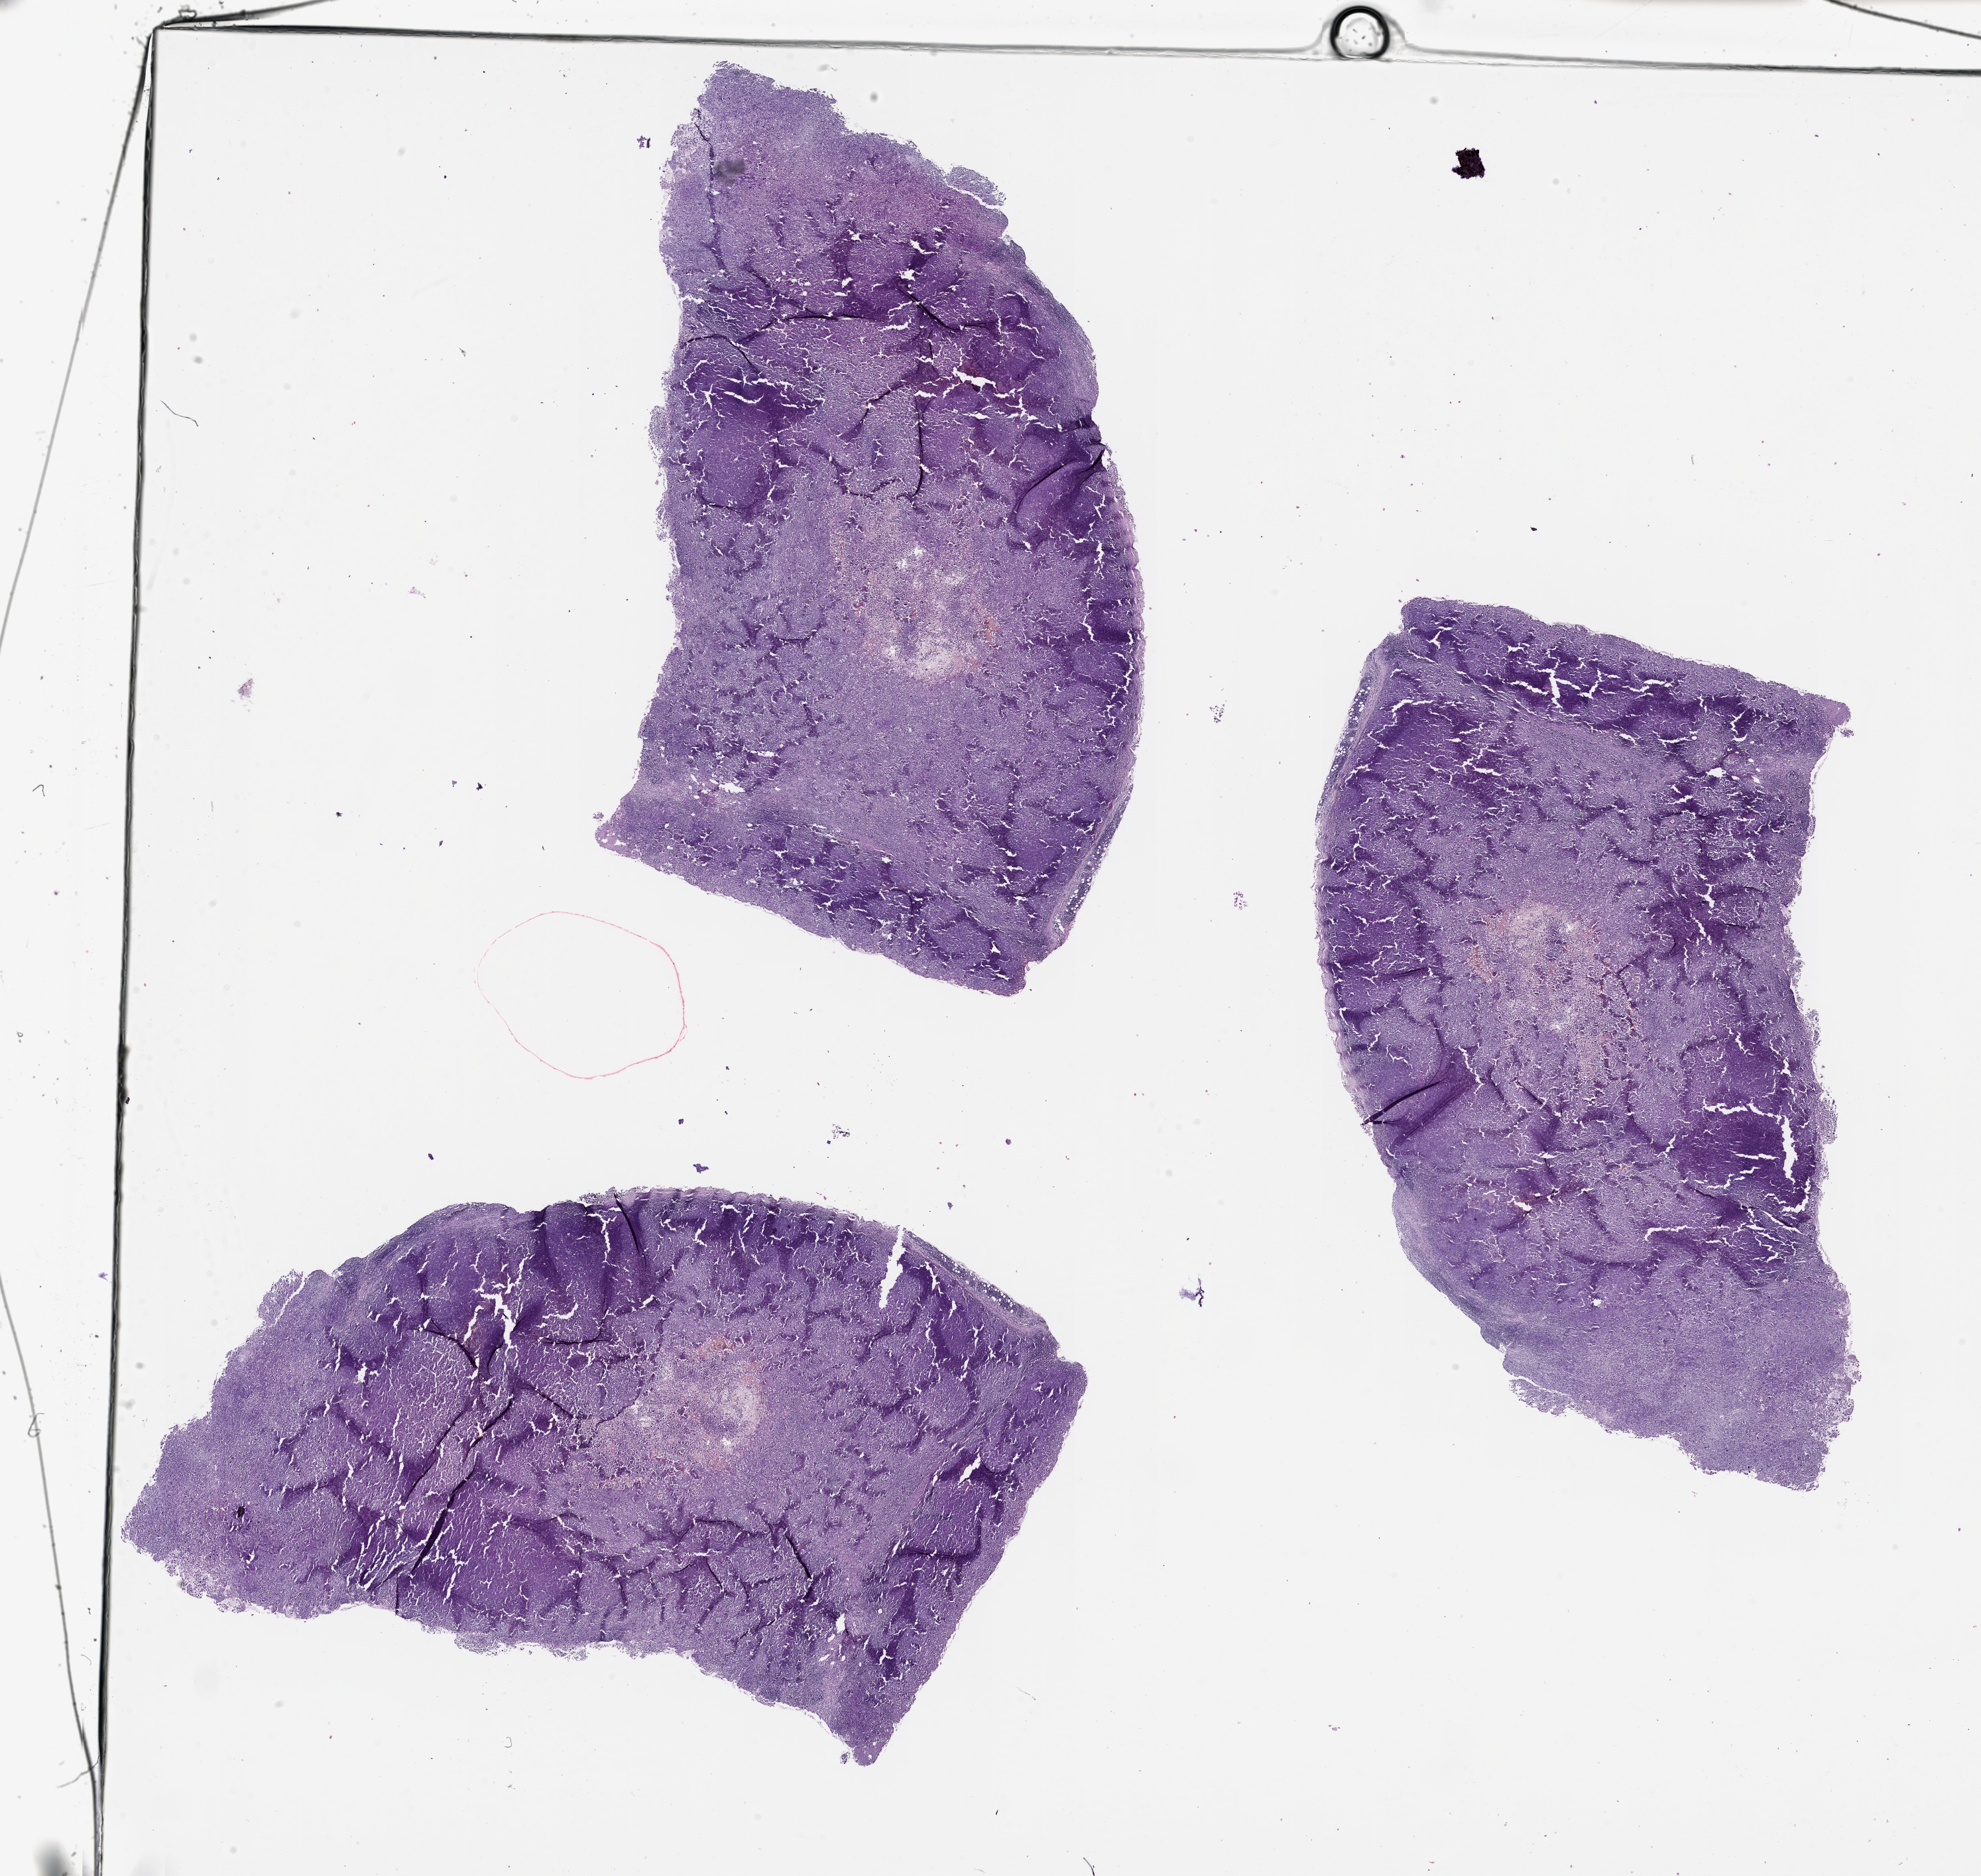
Whole-slide histology image, Hematoxylin and eosin (H&E) stained — whole scanned area (about 24.1 x 22.8 mm, slide scanned at 20x) shown as a low-resolution overview. Tumour tissue sample, sampled site: trunk. Male, 47 y/o. Pathologist review of this section (percent, as recorded): tumour nuclei 80%, necrosis 0%.
This section: metastatic tumour tissue. Patient diagnosis: Malignant melanoma, NOS.